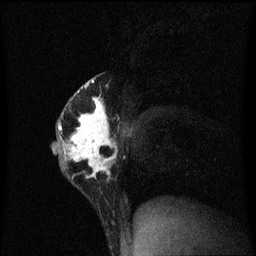
Breast MRI (dynamic contrast-enhanced), one sagittal slice; slice 37 of 60 in the series (ordered by position); dynamic contrast-enhanced series, image 2 of 3 at this slice position (ordered by acquisition); 1.5 T; TE 4.2 ms, TR 8.4 ms; 2 mm slice thickness; 256 × 256 image matrix, field of view 200 × 200 mm. Female patient, age 40 years.
Outlined on this slice (semi-automatic segmentation, software-assisted and operator-edited):
- analysis volume of interest (the breast-tissue region the enhancement analysis was run in; not a lesion): bounding box [x1, y1, x2, y2] px = [53, 74, 118, 201]
- tumour enhancement mask (voxels above the 70 % enhancement threshold inside the analysis volume of interest): [59, 80, 118, 179]